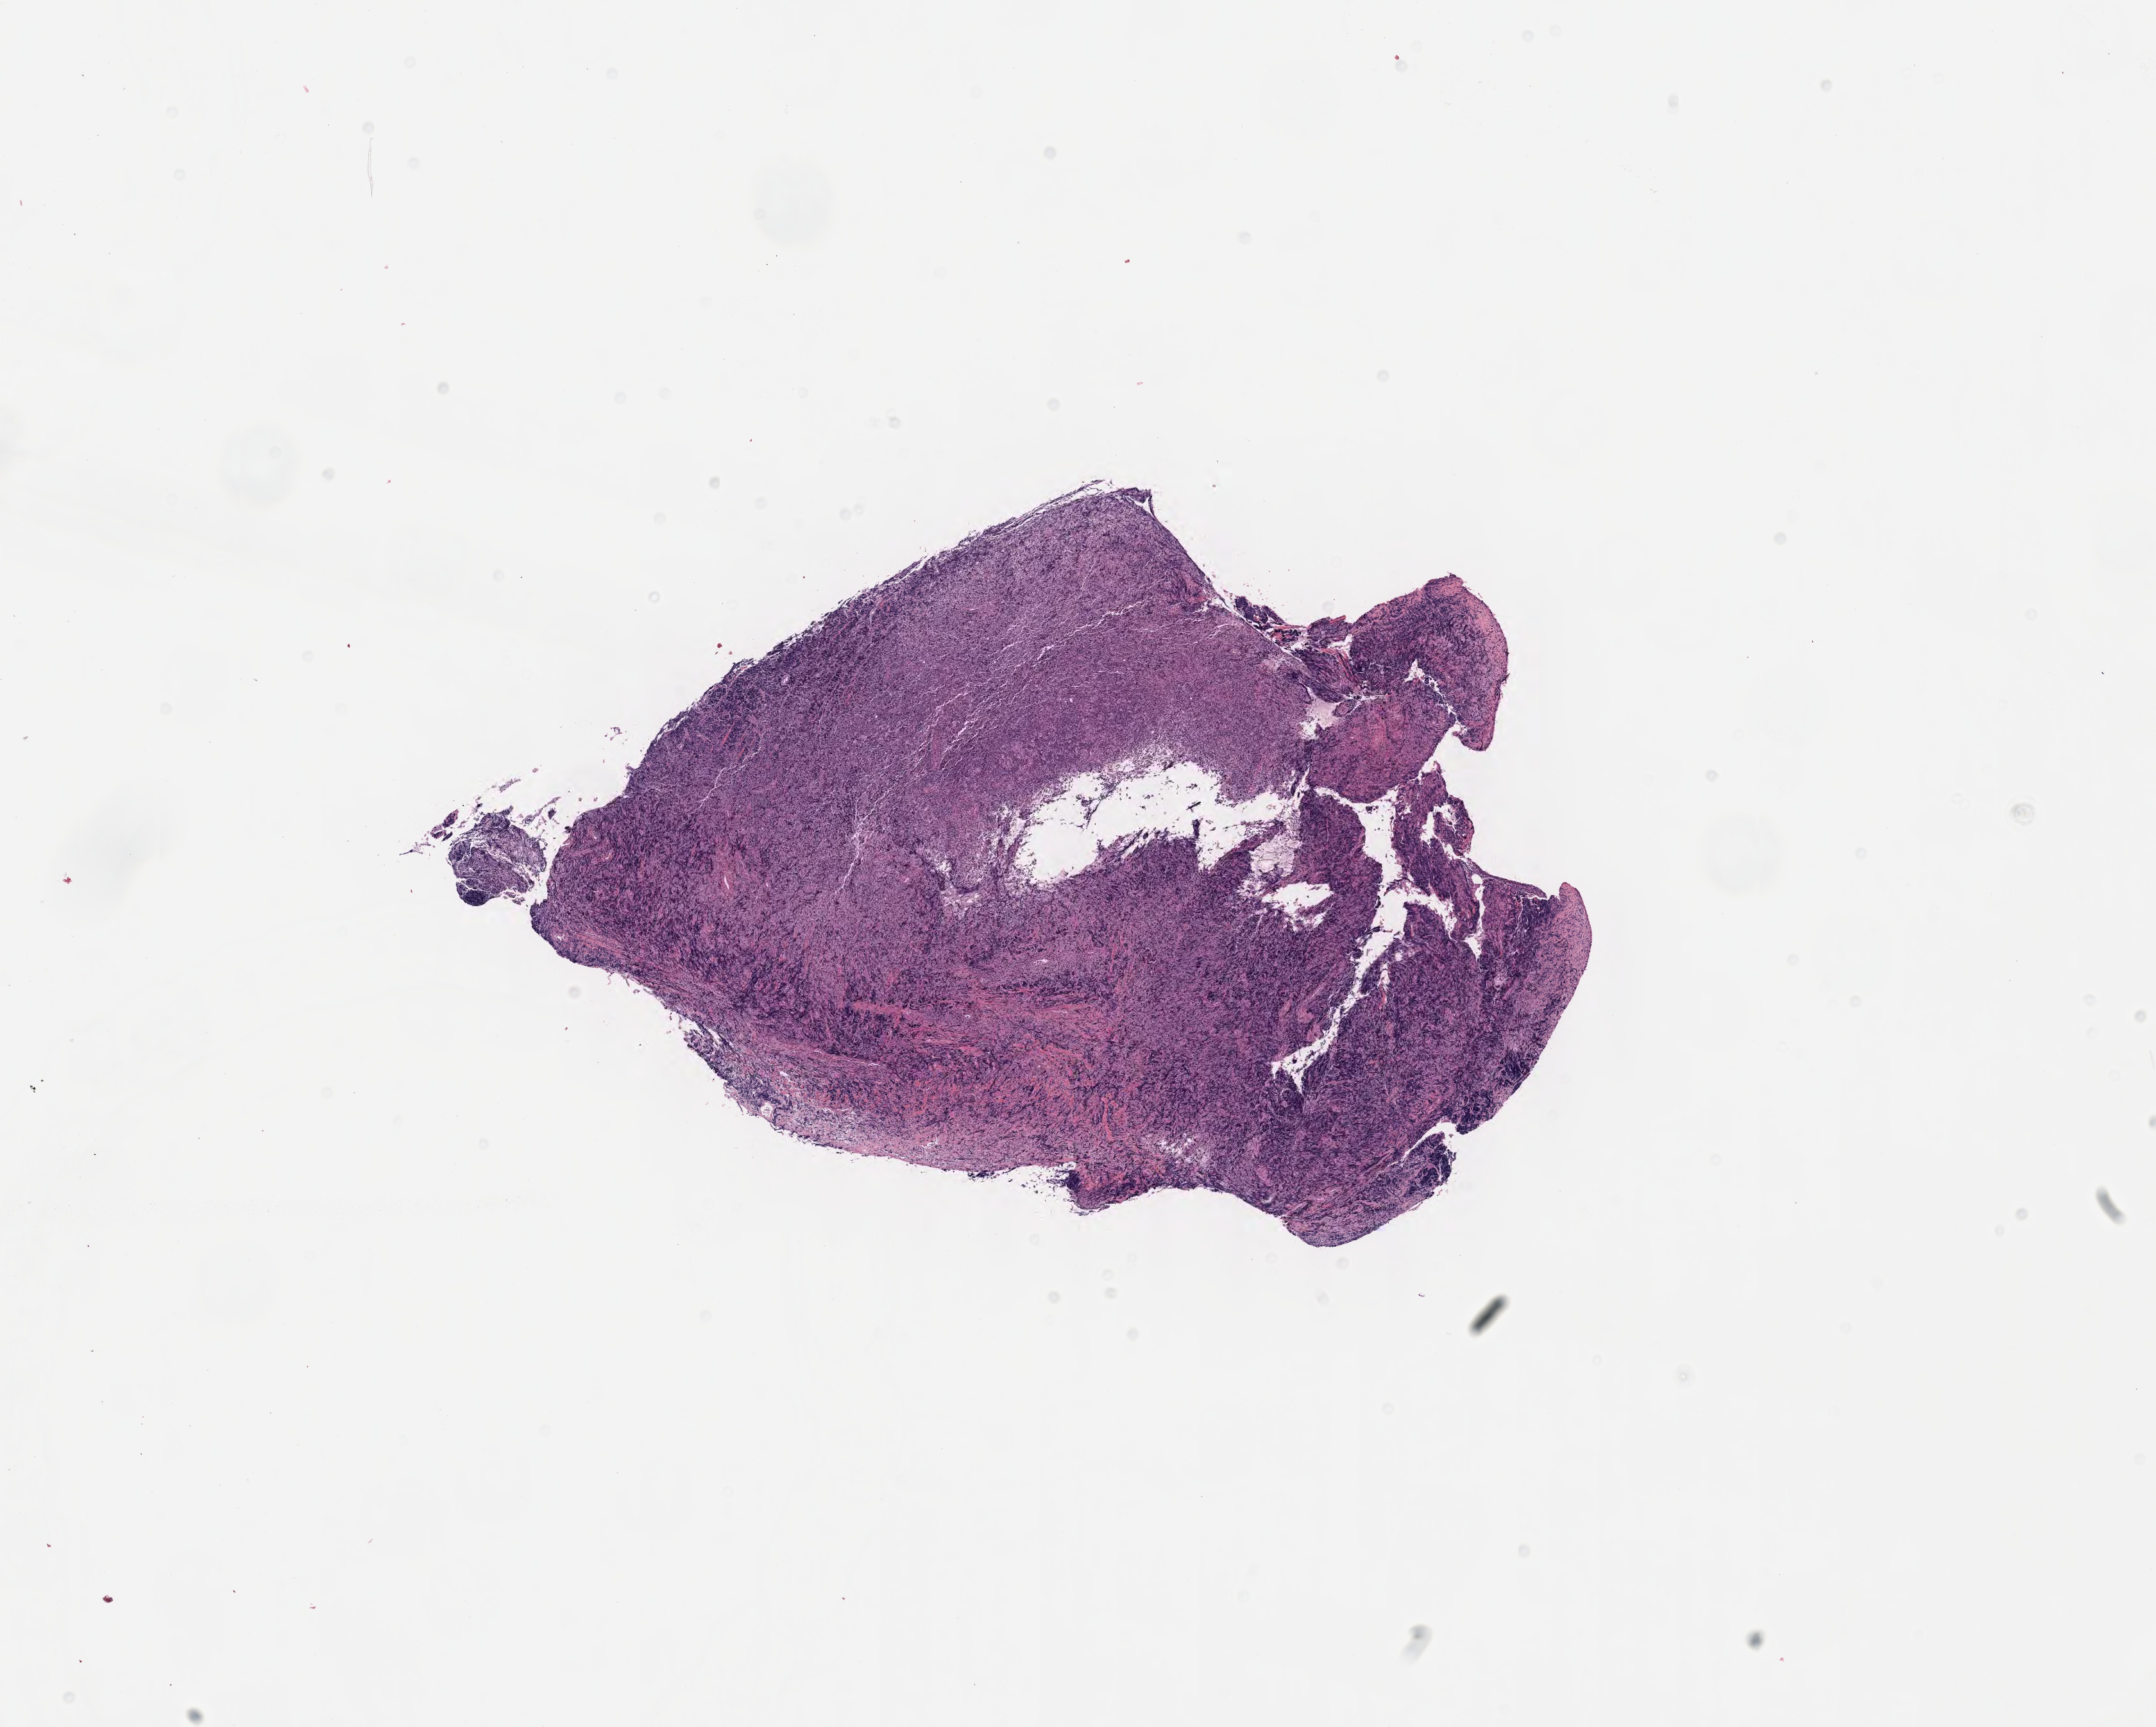
Whole-slide image, H&E stain — shown as a low-resolution overview of the whole scanned area (about 13.6 x 10.9 mm), specimen: tumor tissue, anatomic site: ovary. Female, age 3 years at initial diagnosis.
Diagnosis: Burkitt lymphoma, NOS.